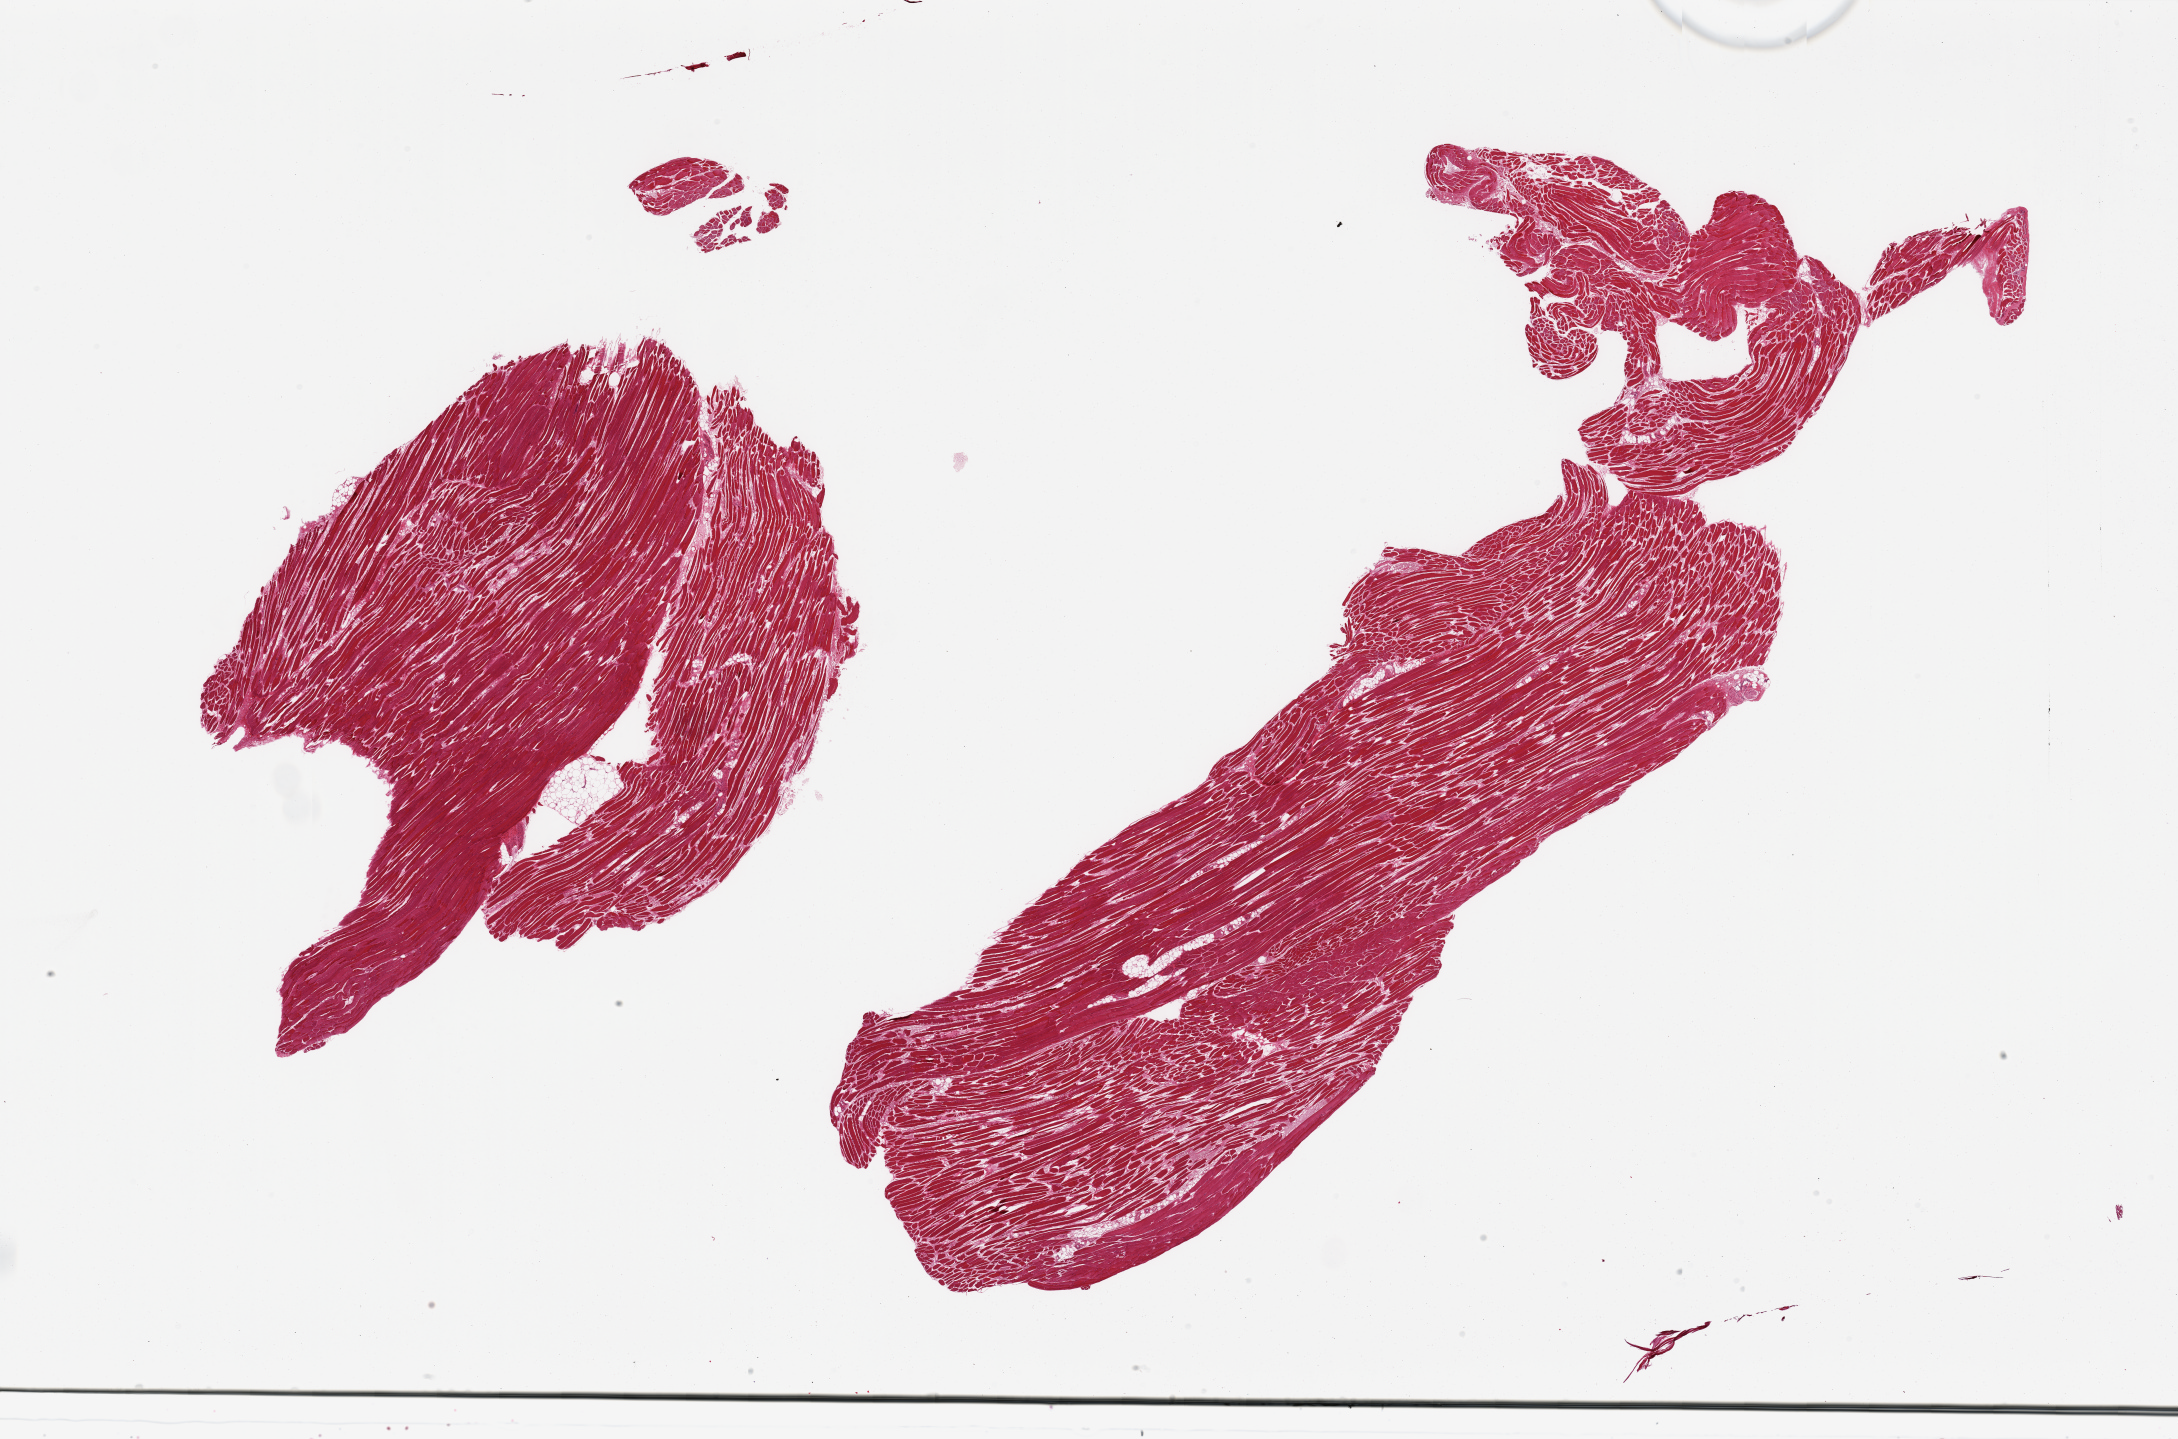
Digitized hematoxylin and eosin (H&E)-stained section, a low-resolution overview of the entire scanned area, about 34.5 x 22.8 mm (slide scanned at 20x); PAXgene-fixed, paraffin-embedded tissue; section of skeletal muscle (target tissue); donor tissue sample.
Reviewer comment on this tissue sample: 2 pieces; striations clearly visible.